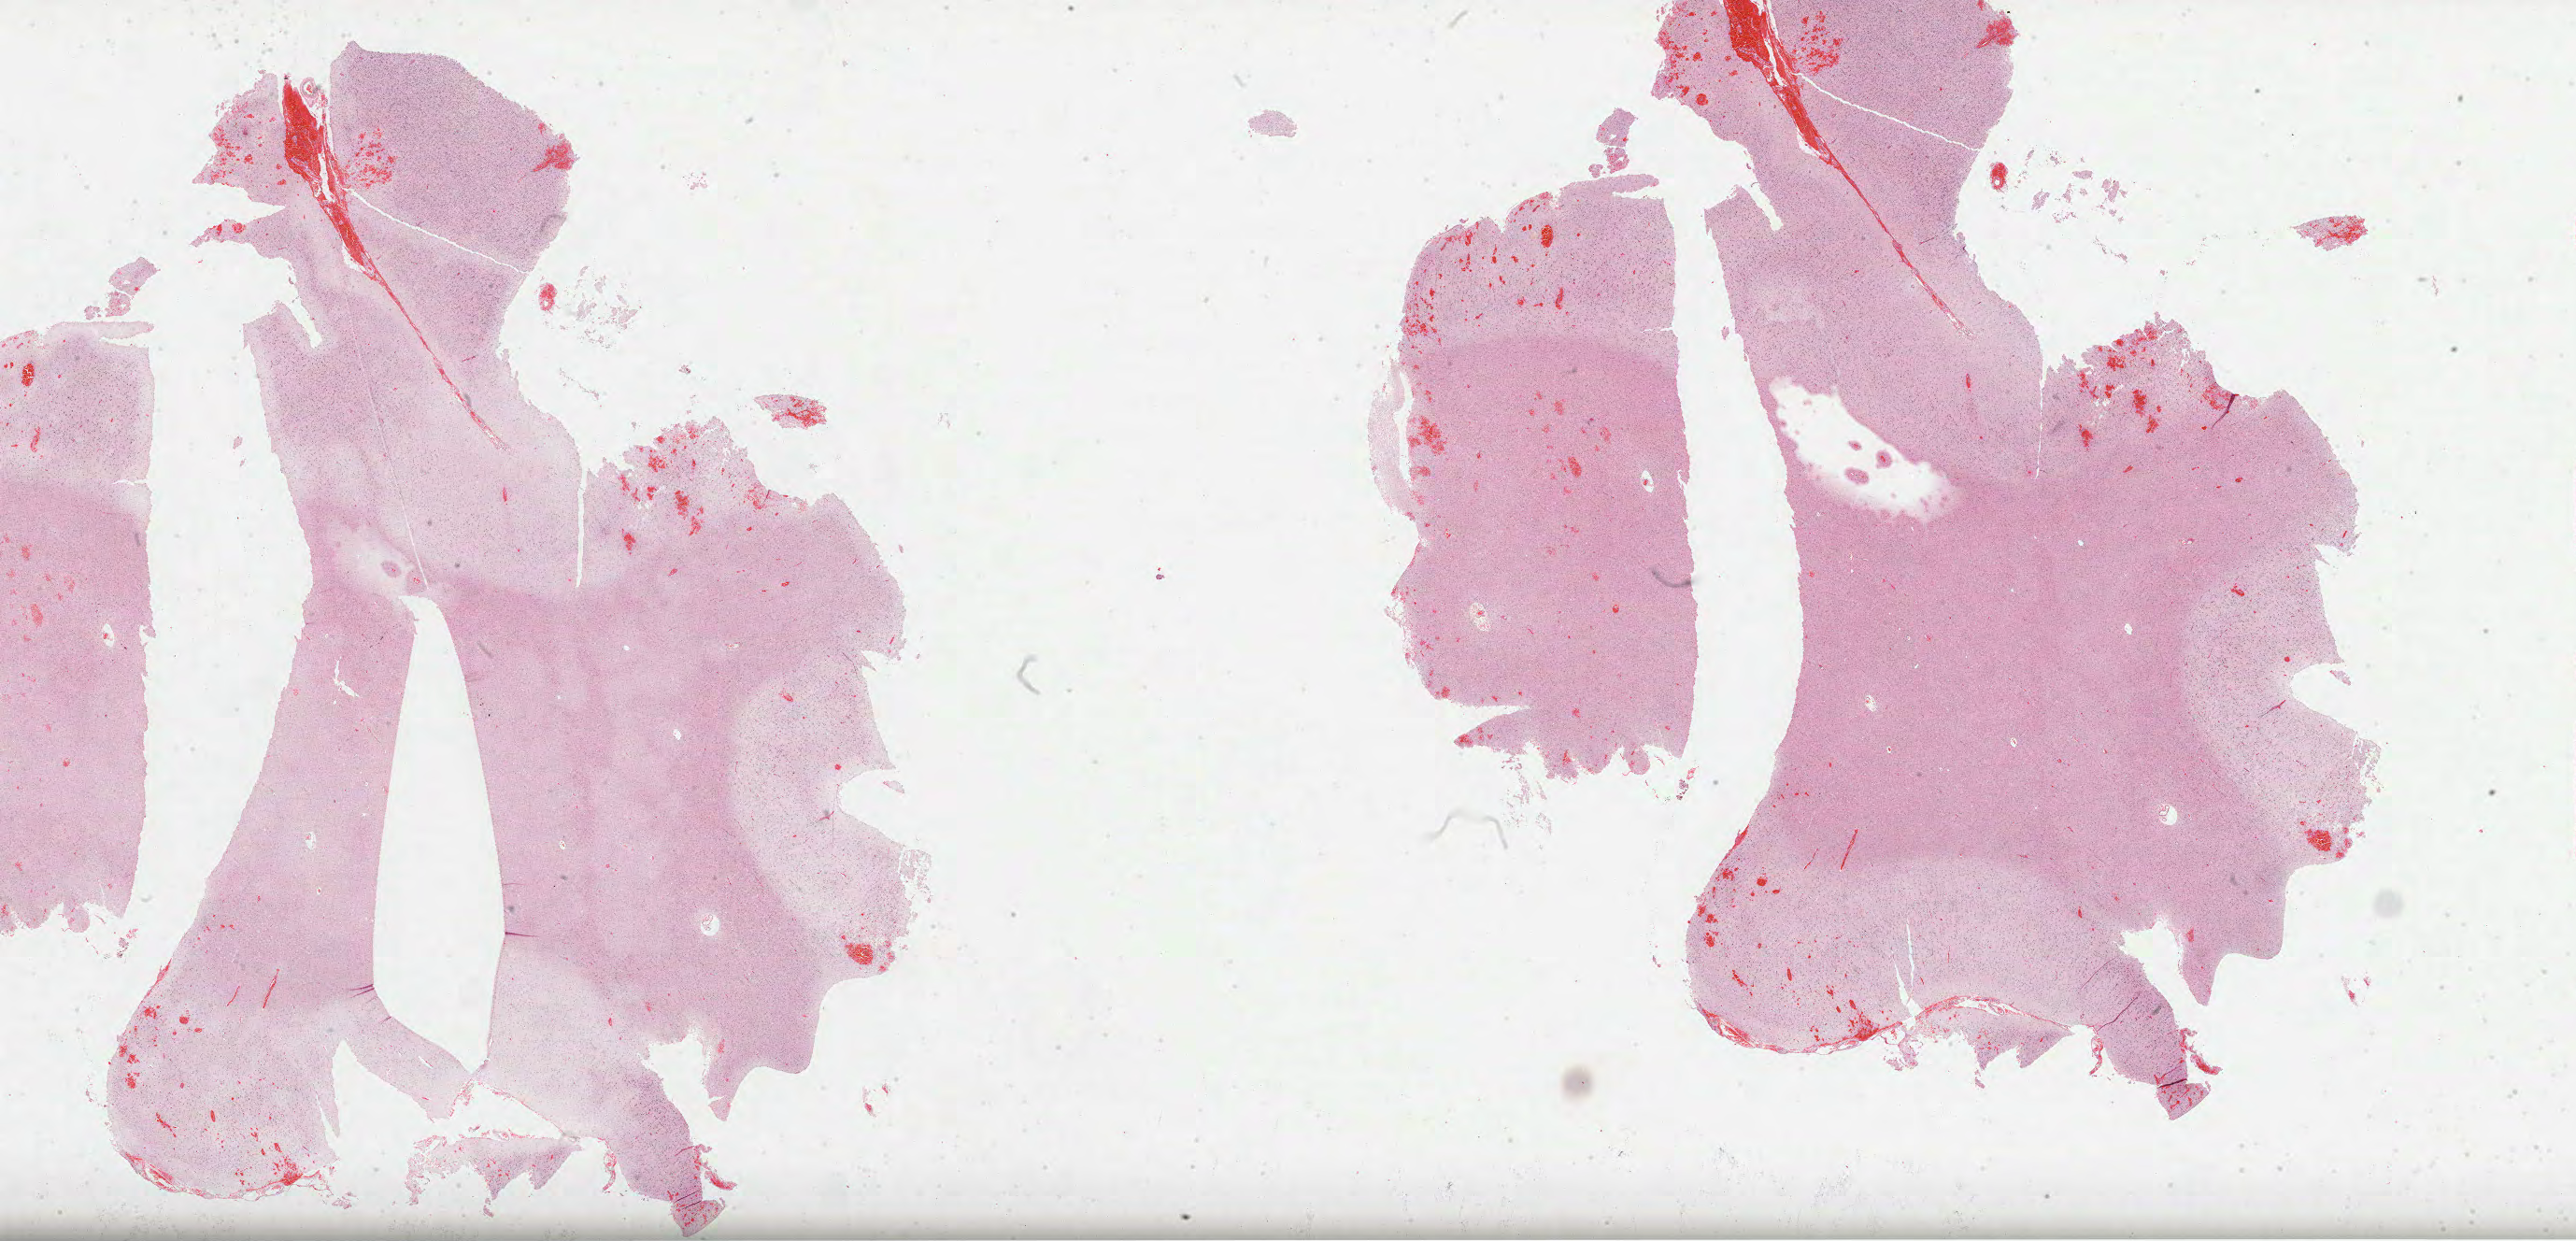
Whole-slide histology image, H&E-stained — a low-resolution overview of the entire scanned area, about 44.5 x 21.4 mm (from a 40x scan), FFPE section, sample: primary tumour, brain. Female patient; age at initial diagnosis 59 years. Histologic grade: G3 (poorly differentiated).
Laterality: left. Pathologic diagnosis: Astrocytoma, anaplastic (cerebrum).